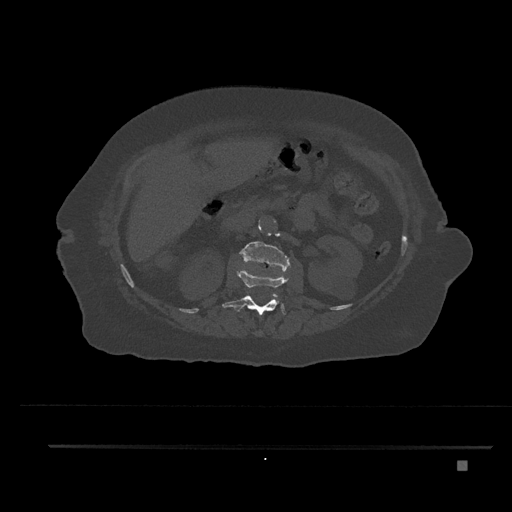
CT including the spine, one axial slice. Slice 211 of 797 in the series (ordered by position). Reconstruction kernel Br40s/3. 120 kVp. Bone window (W 1800 / L 400 HU). 512 × 512 image matrix. Female patient, age 76 years. Case-level facts recorded for this patient, not image findings: primary cancer: lung.
Outlined on this slice (semi-automatically segmented with operator editing):
- L1 vertebra: bounding box [x1, y1, x2, y2] px = [222, 269, 289, 318]
- L2 vertebra: [239, 241, 290, 296]